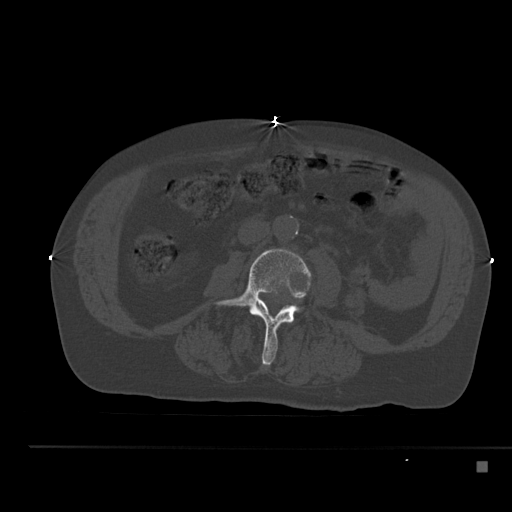
CT including the spine, one axial slice. Position 162 of 517 along the scan axis. Reconstruction kernel Br40s. Bone window (W 1800 / L 400 HU). 1.5 mm slice thickness. 512 × 512 image matrix. Patient: male, 70 years. From the clinical record (not read from this slice): primary cancer: renal; vertebrae with lytic lesions (as recorded): T4, T6, T10, T12, L3, L4, L5.
Structures marked on this image (semi-automatically segmented with operator editing):
- L3 vertebra: bounding box <215,249,311,366> (left, top, right, bottom; pixels)